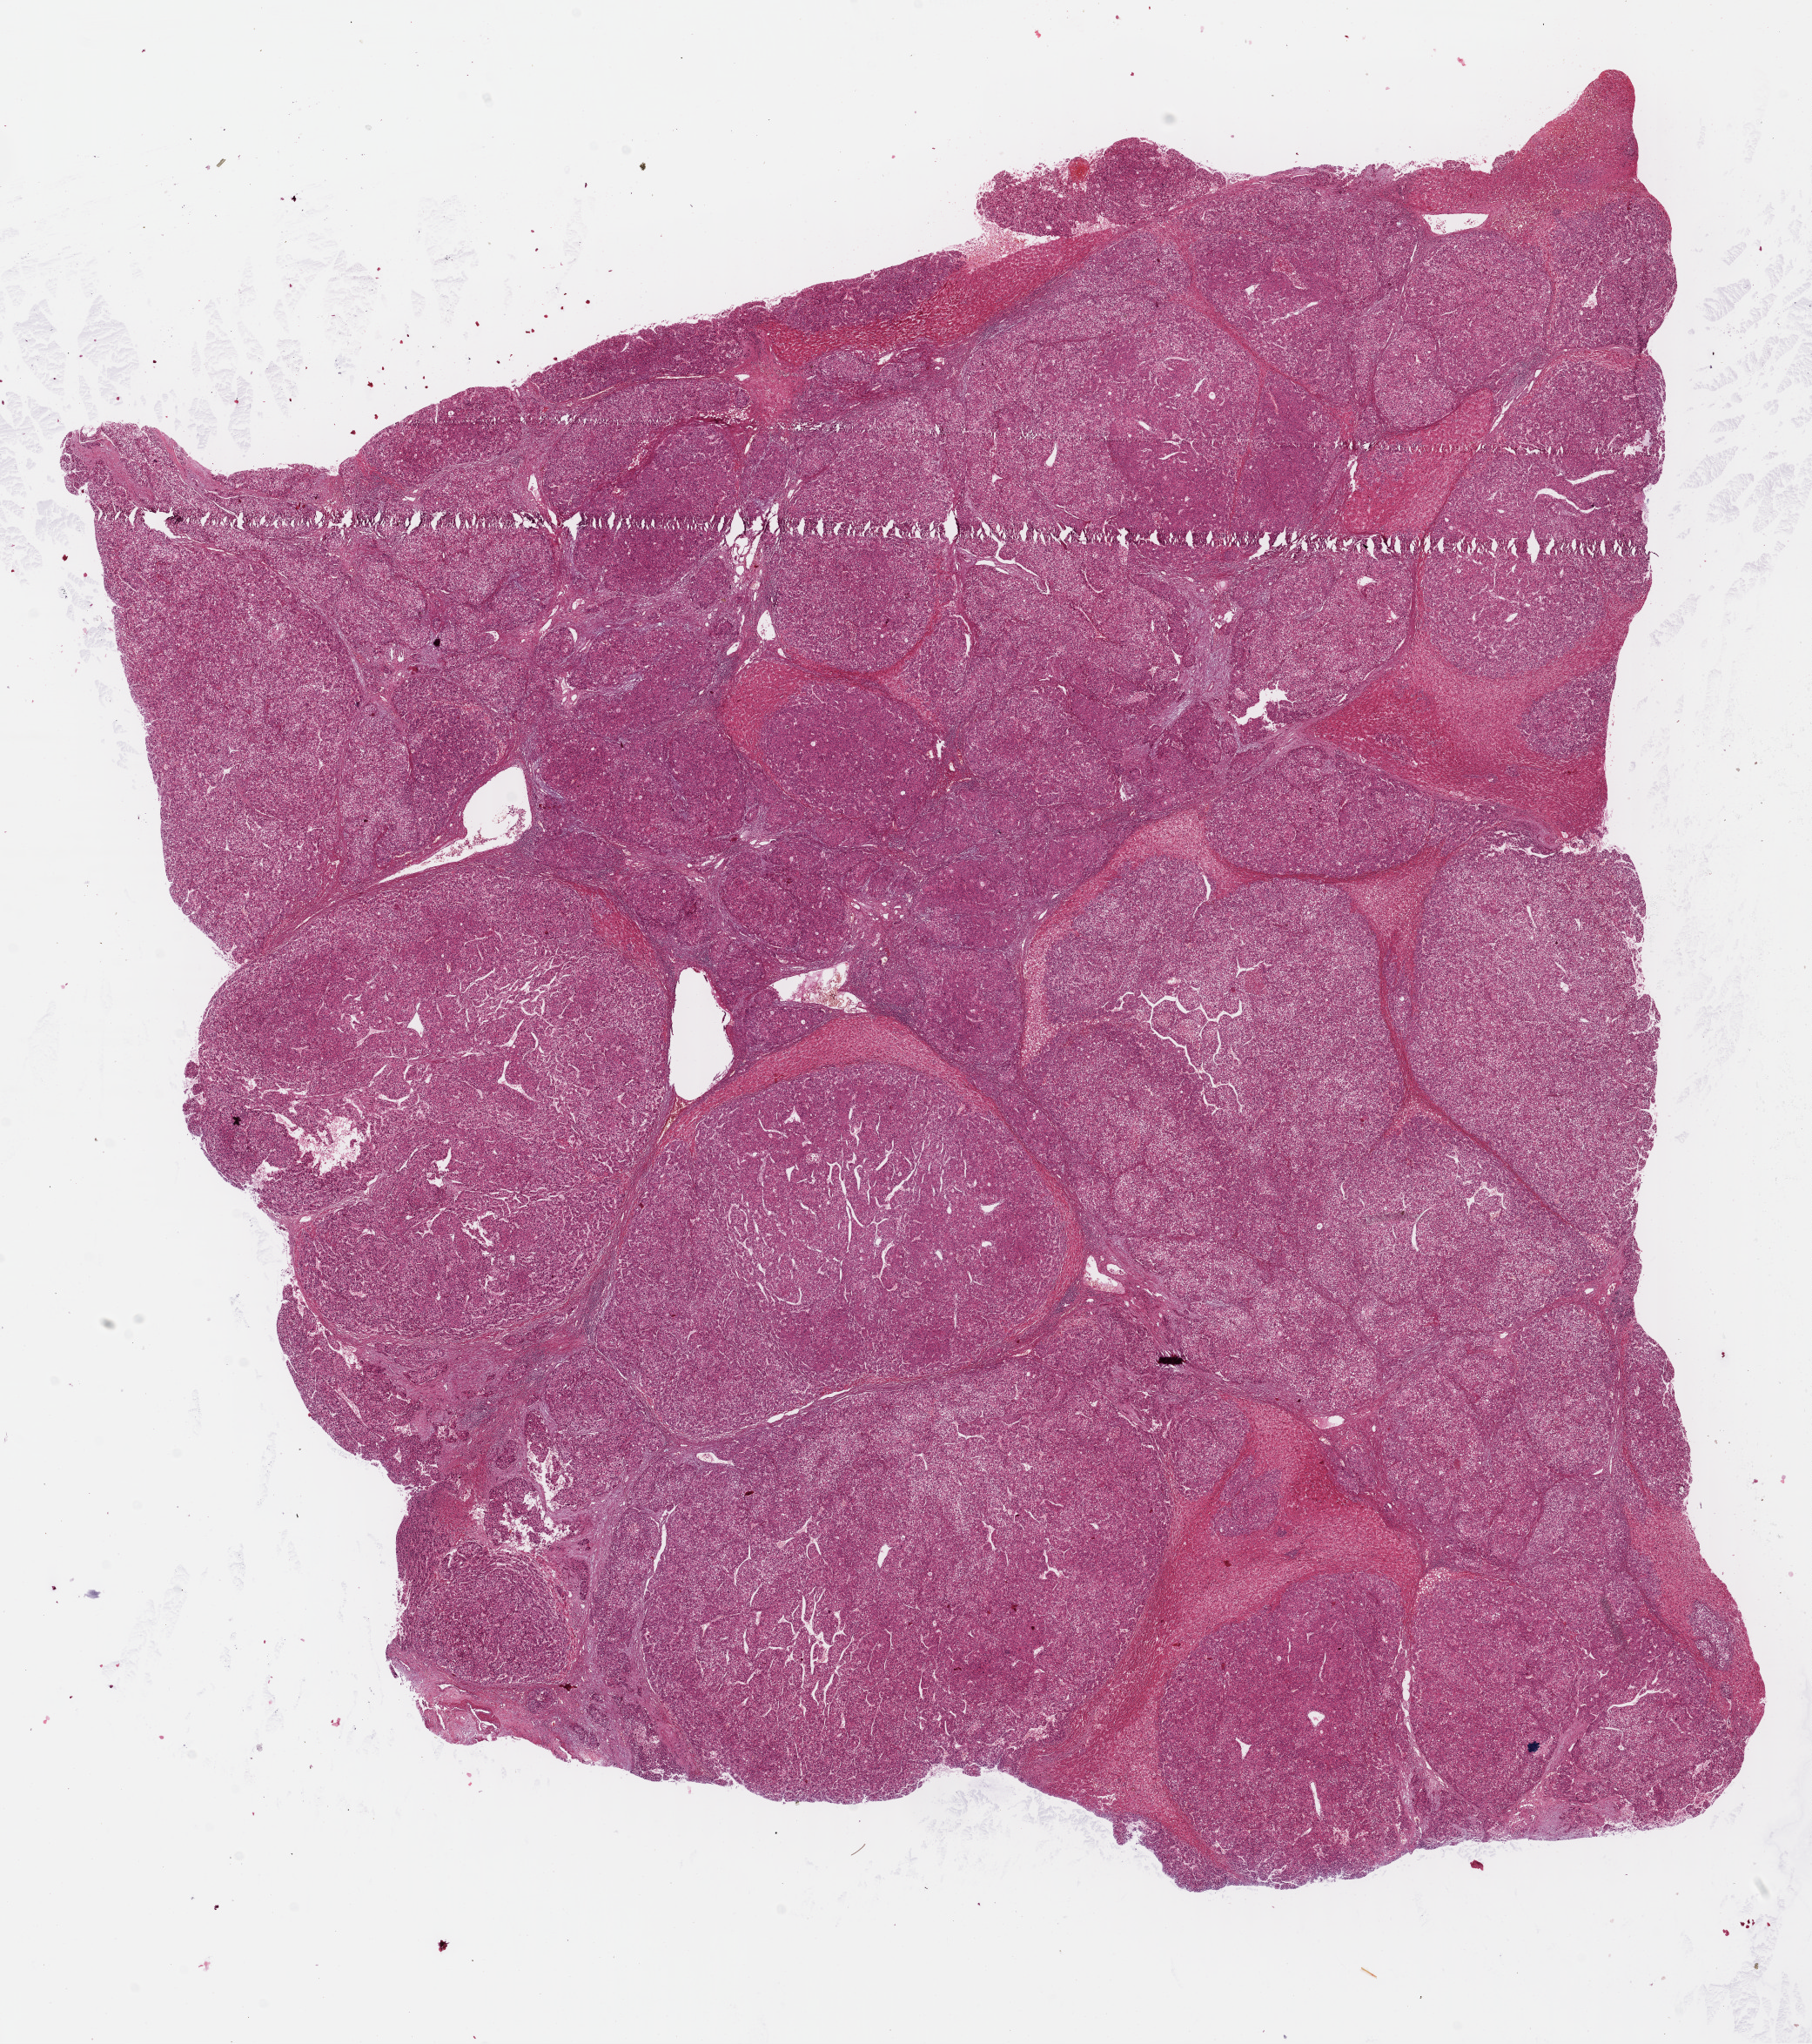
H&E whole-slide image — low-resolution overview of the scanned area, about 16.4 x 18.5 mm, FFPE section, liver, primary tumour sample. Patient: male, age at initial diagnosis 36 years.
Histologic diagnosis: Hepatocellular carcinoma, NOS.